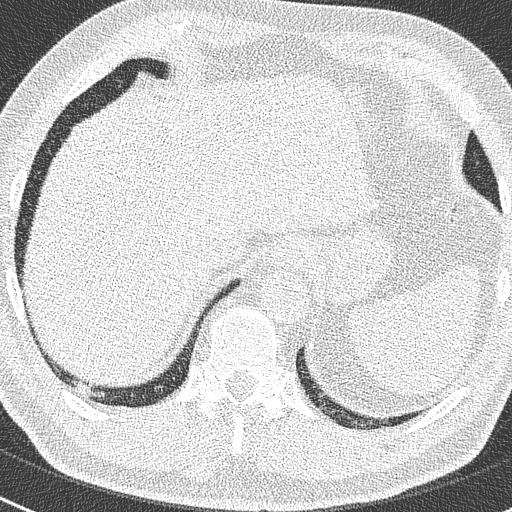
Chest CT (low-dose screening protocol), one axial image; second screening round (one year after baseline); lung window (W 1500 / L -600 HU); 2 mm slice thickness; 120 kVp; 512 × 512 image matrix, field of view 300 × 300 mm. Male participant, aged 63 years at enrolment.
• Expert reader's lesion annotation, bounding box (x1, y1, x2, y2) in pixels: (67, 378, 100, 404).
• No non-calcified nodule or mass ≥4 mm was recorded by the screening reader at this exam.